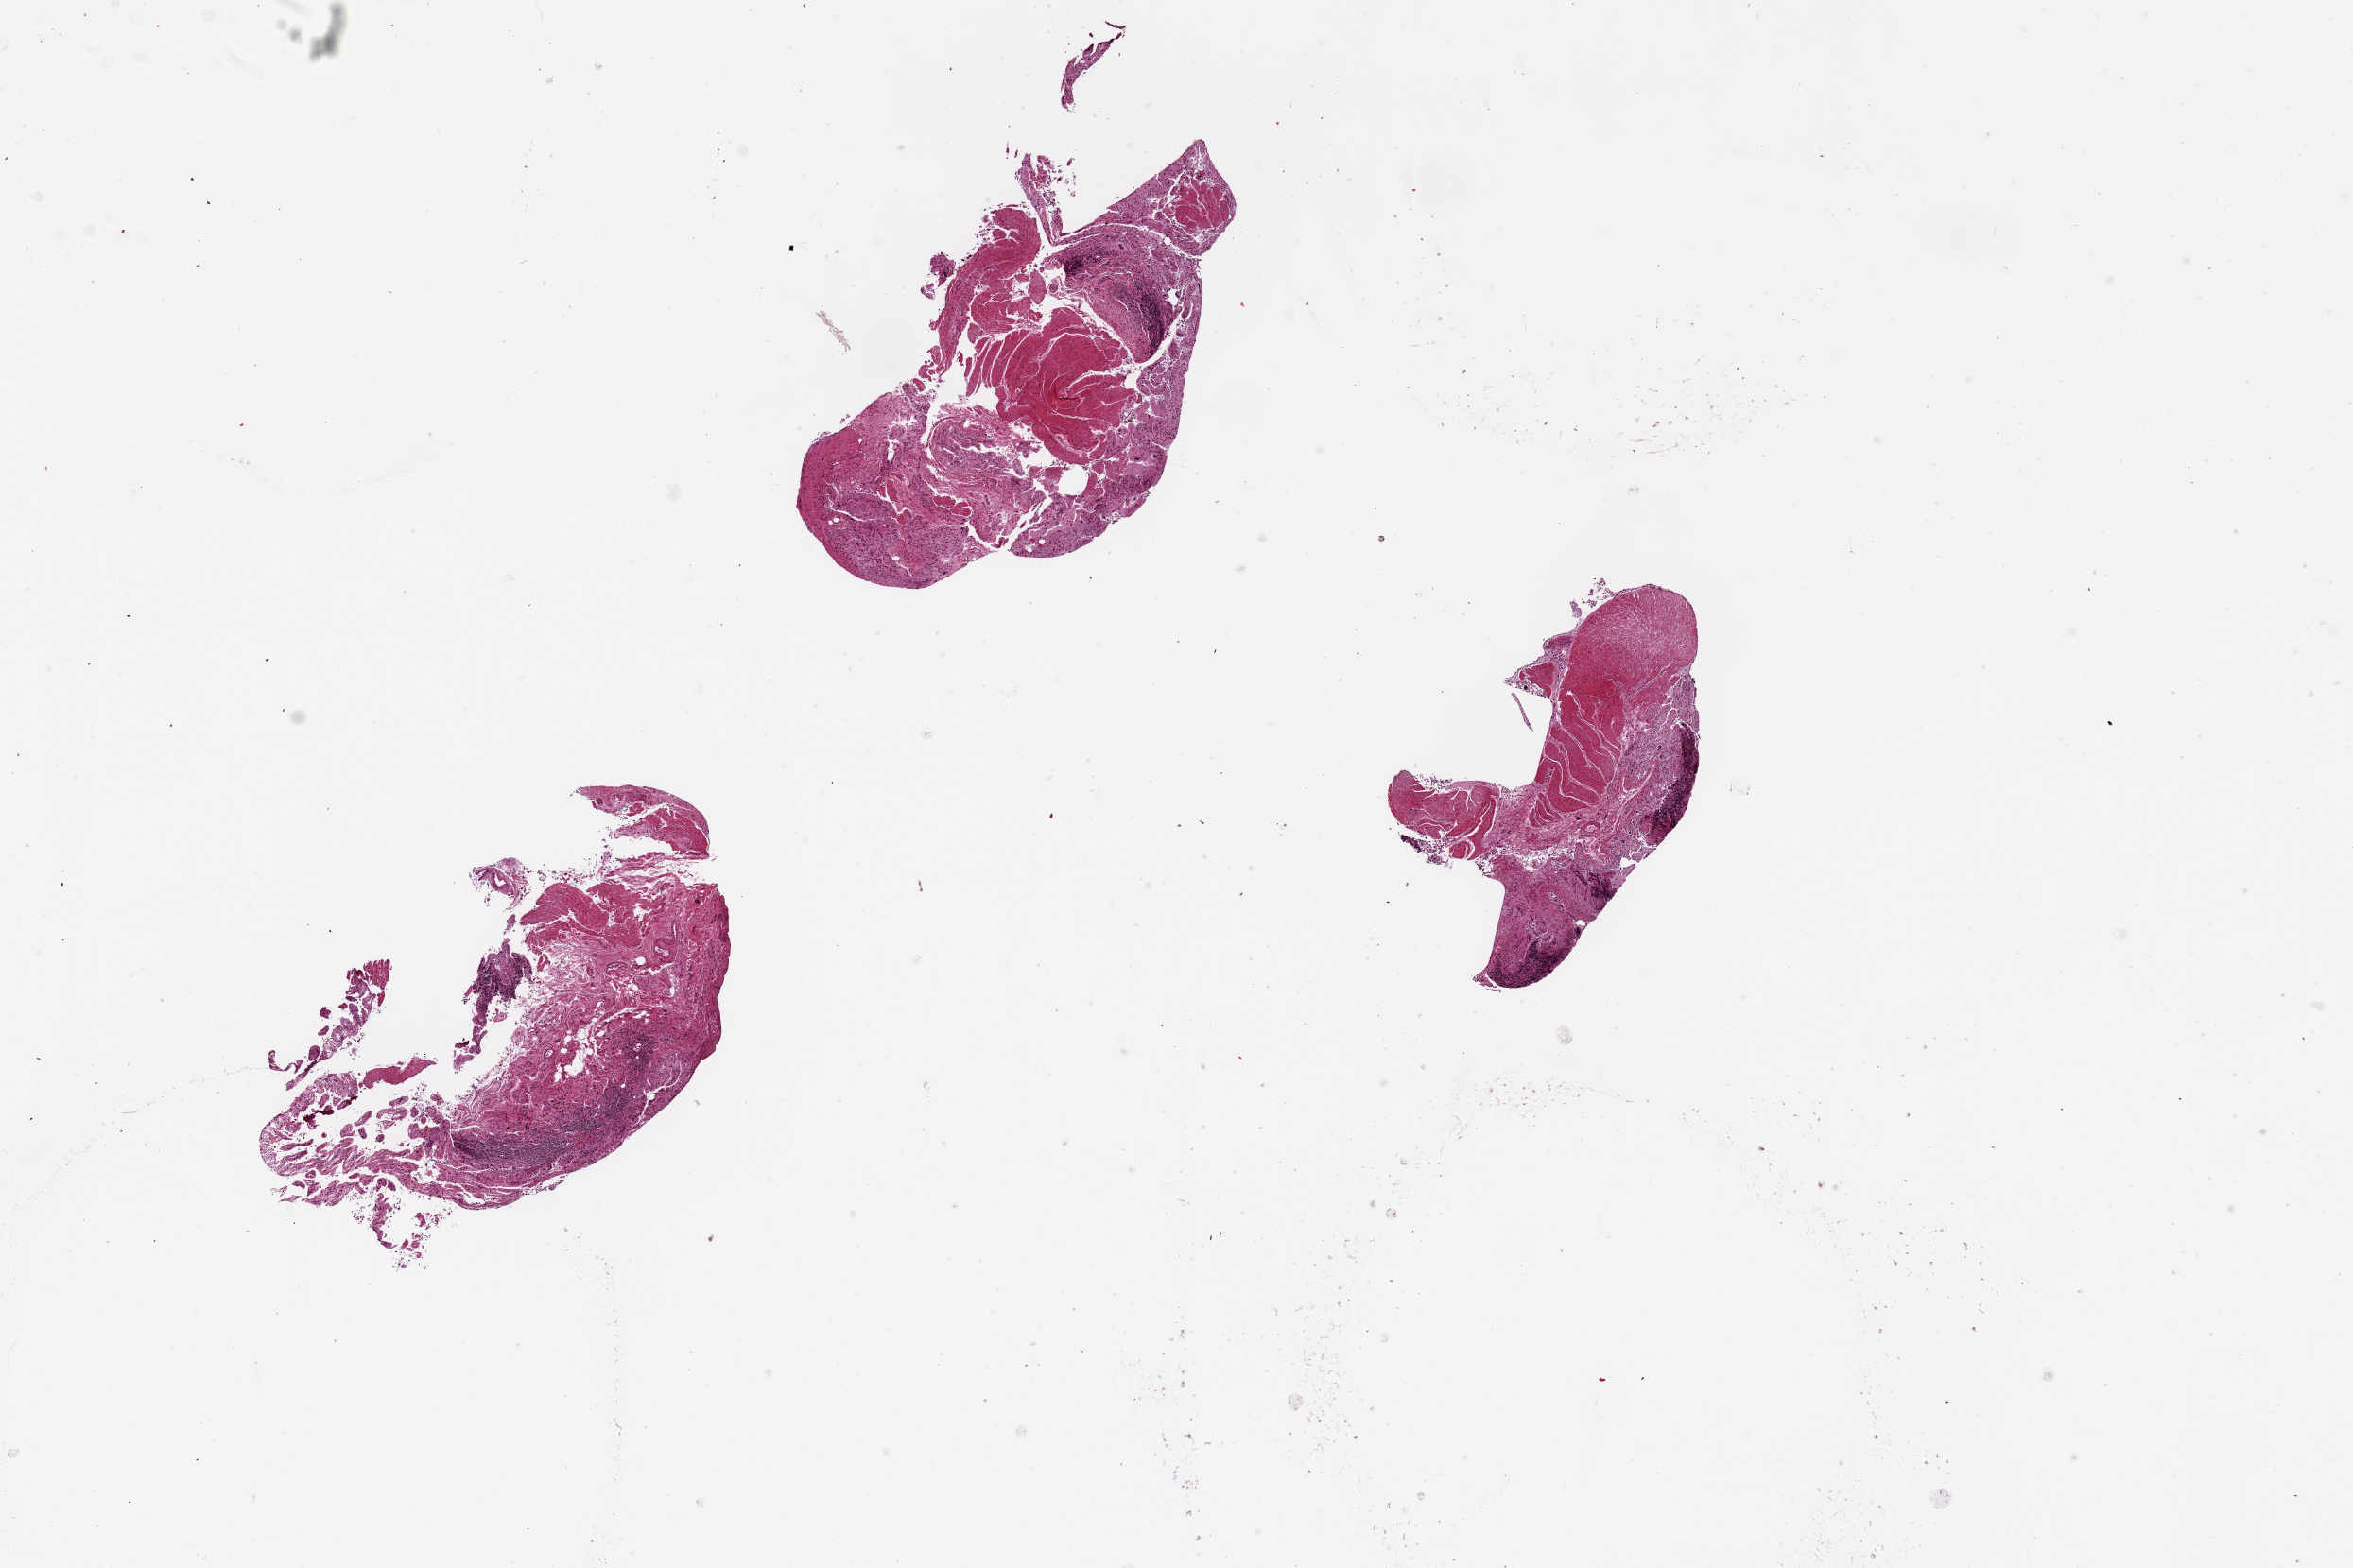
Digitized hematoxylin and eosin (H&E)-stained section, whole scanned area (about 19.7 x 13.1 mm, slide scanned at 20x) shown as a low-resolution overview, PAXgene-fixed, paraffin-embedded tissue, target tissue: ileum, tissue donor sample. Donor: female.
Review note (as recorded): 3 pieces, up to 5x2.5mm; badly autolyzed, lymphoid elements, ~10% total volume.